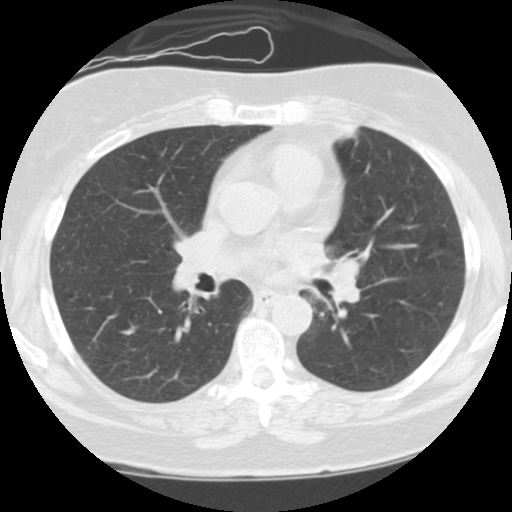
Axial slice from a low-dose chest CT screening exam. Third annual screen. Lung window (W 1500 / L -600 HU). 2.5 mm slice thickness. Standard (soft-tissue) reconstruction kernel (STANDARD). 120 kVp. 512 × 512 image matrix, field of view 300 × 300 mm. Female participant, aged 59 years at enrolment.
Lesion marked by an expert reader, bounding box (x1, y1, x2, y2) in pixels: (285, 213, 391, 325). Screening reader's record for this exam: no non-calcified nodule ≥4 mm recorded. Official screen result: positive, other. Participant outcome: lung cancer diagnosed 192 days after this screen — small cell carcinoma, NOS, left upper lobe, left hilum, mediastinum, left main stem bronchus, stage IV (AJCC 6th edition), 63 mm at pathology.